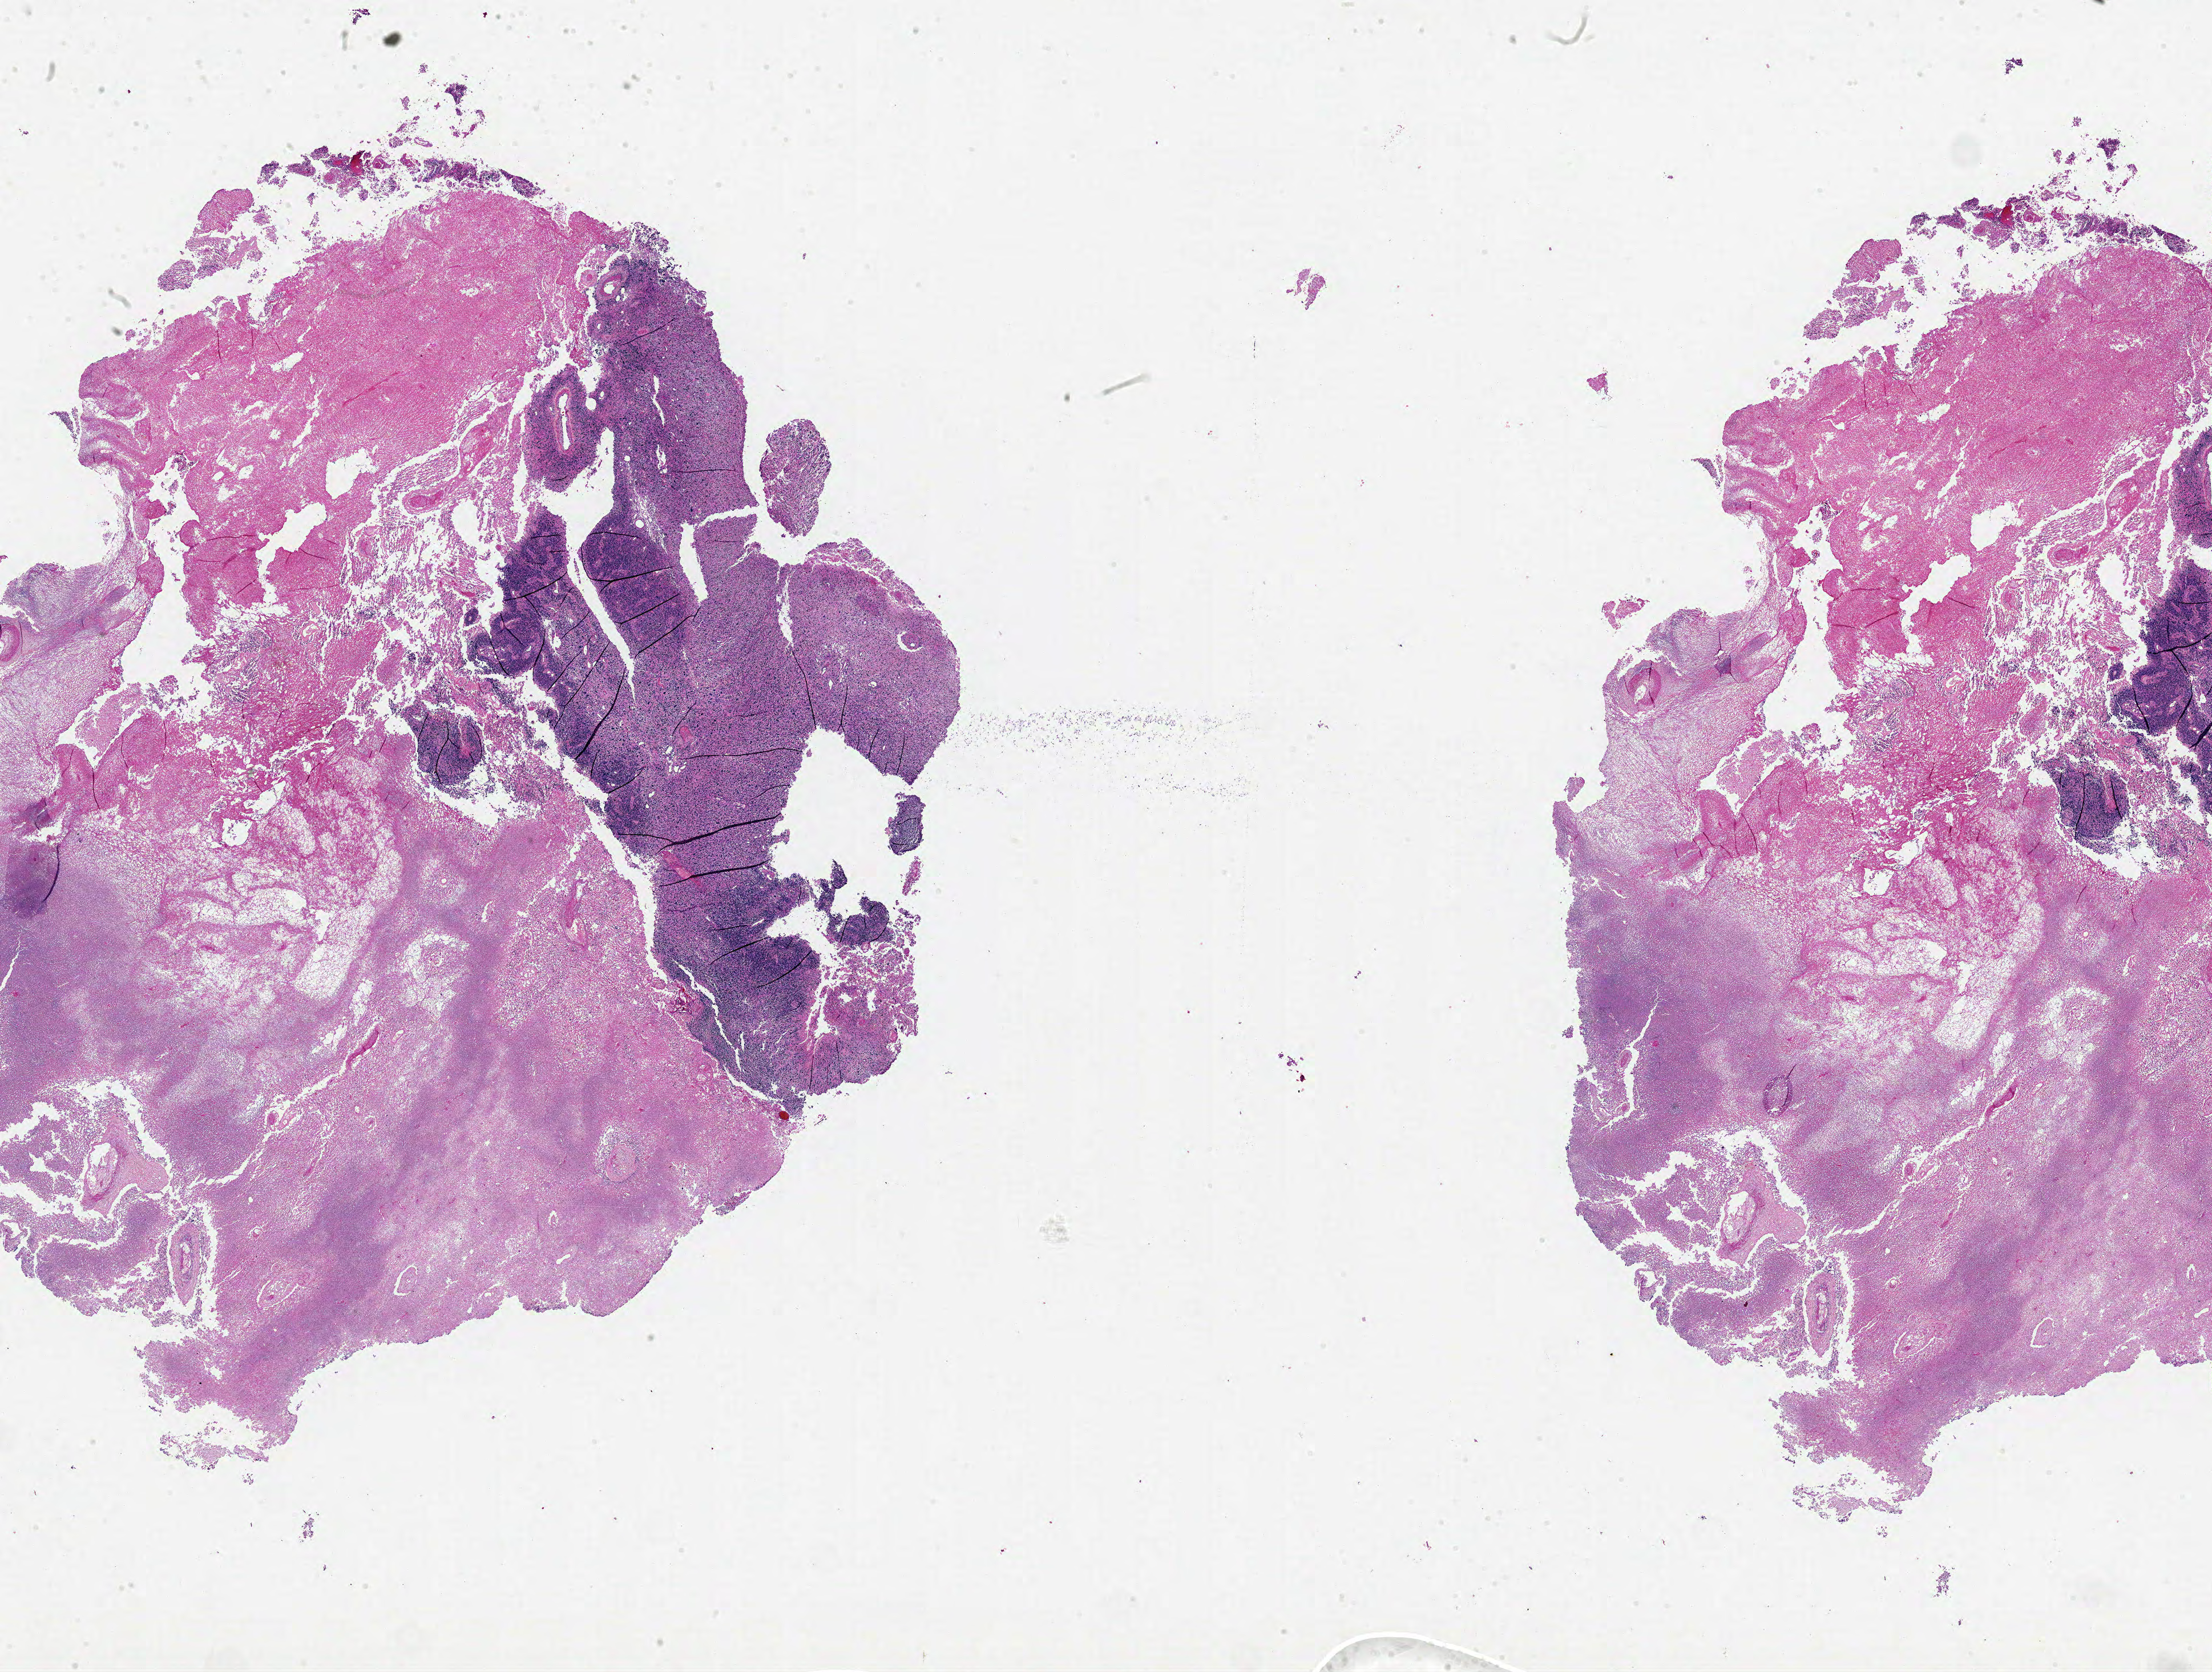
Digitized H&E-stained tissue section (whole slide) — whole scanned area (about 31.0 x 23.4 mm) shown as a low-resolution overview, formalin-fixed paraffin-embedded (FFPE) diagnostic section, brain, primary tumour sample. Female, age 75 years at initial diagnosis.
Histologic diagnosis: Glioblastoma.